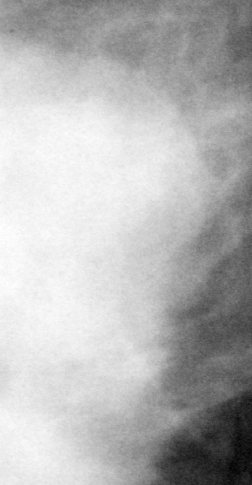
Region of interest cut from a scanned film mammogram (one marked finding); left breast; CC view.
Finding: mass, shape irregular, margins microlobulated; BI-RADS assessment category 5; subtlety rating 5 on a 1 (subtle) to 5 (obvious) scale; pathology (as recorded): malignant.